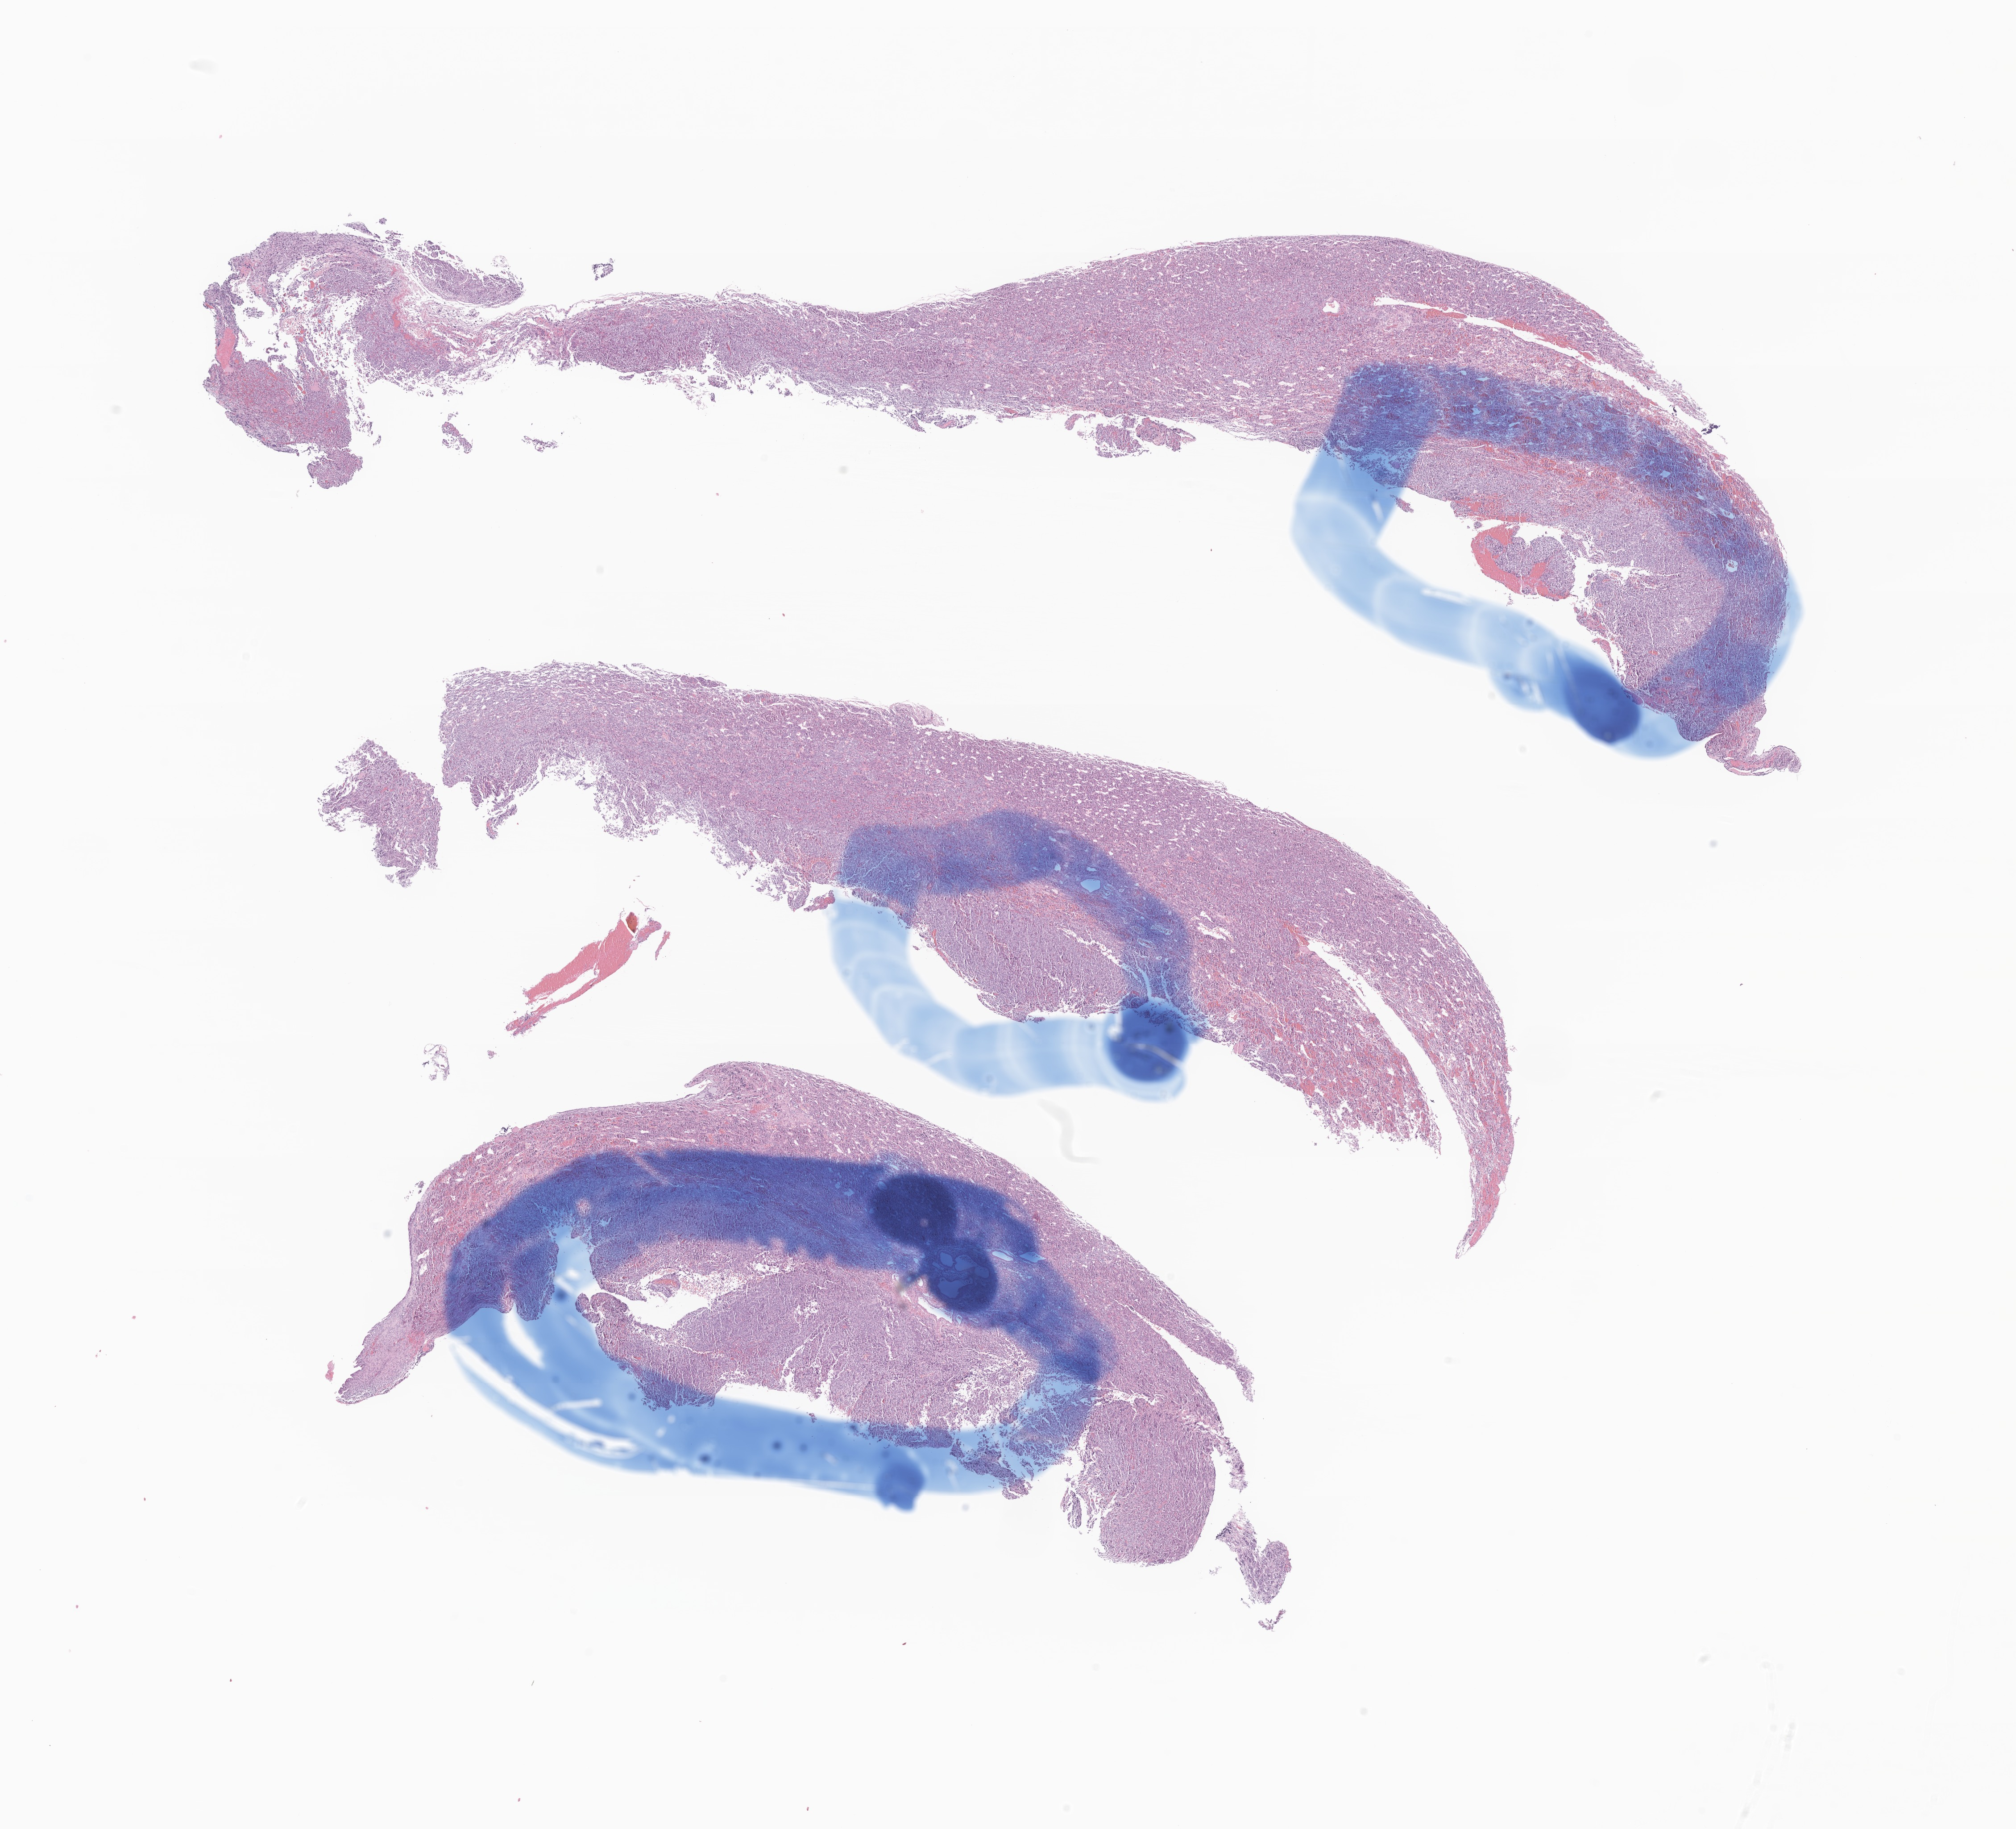
Digitized haematoxylin and eosin-stained section of tumor tissue from the pituitary gland, low-resolution overview of the scanned area, about 19.0 x 17.3 mm. FFPE section. Patient: male, age 221 months (18 years 5 months).
Diagnosis: Pituitary adenoma, NOS.